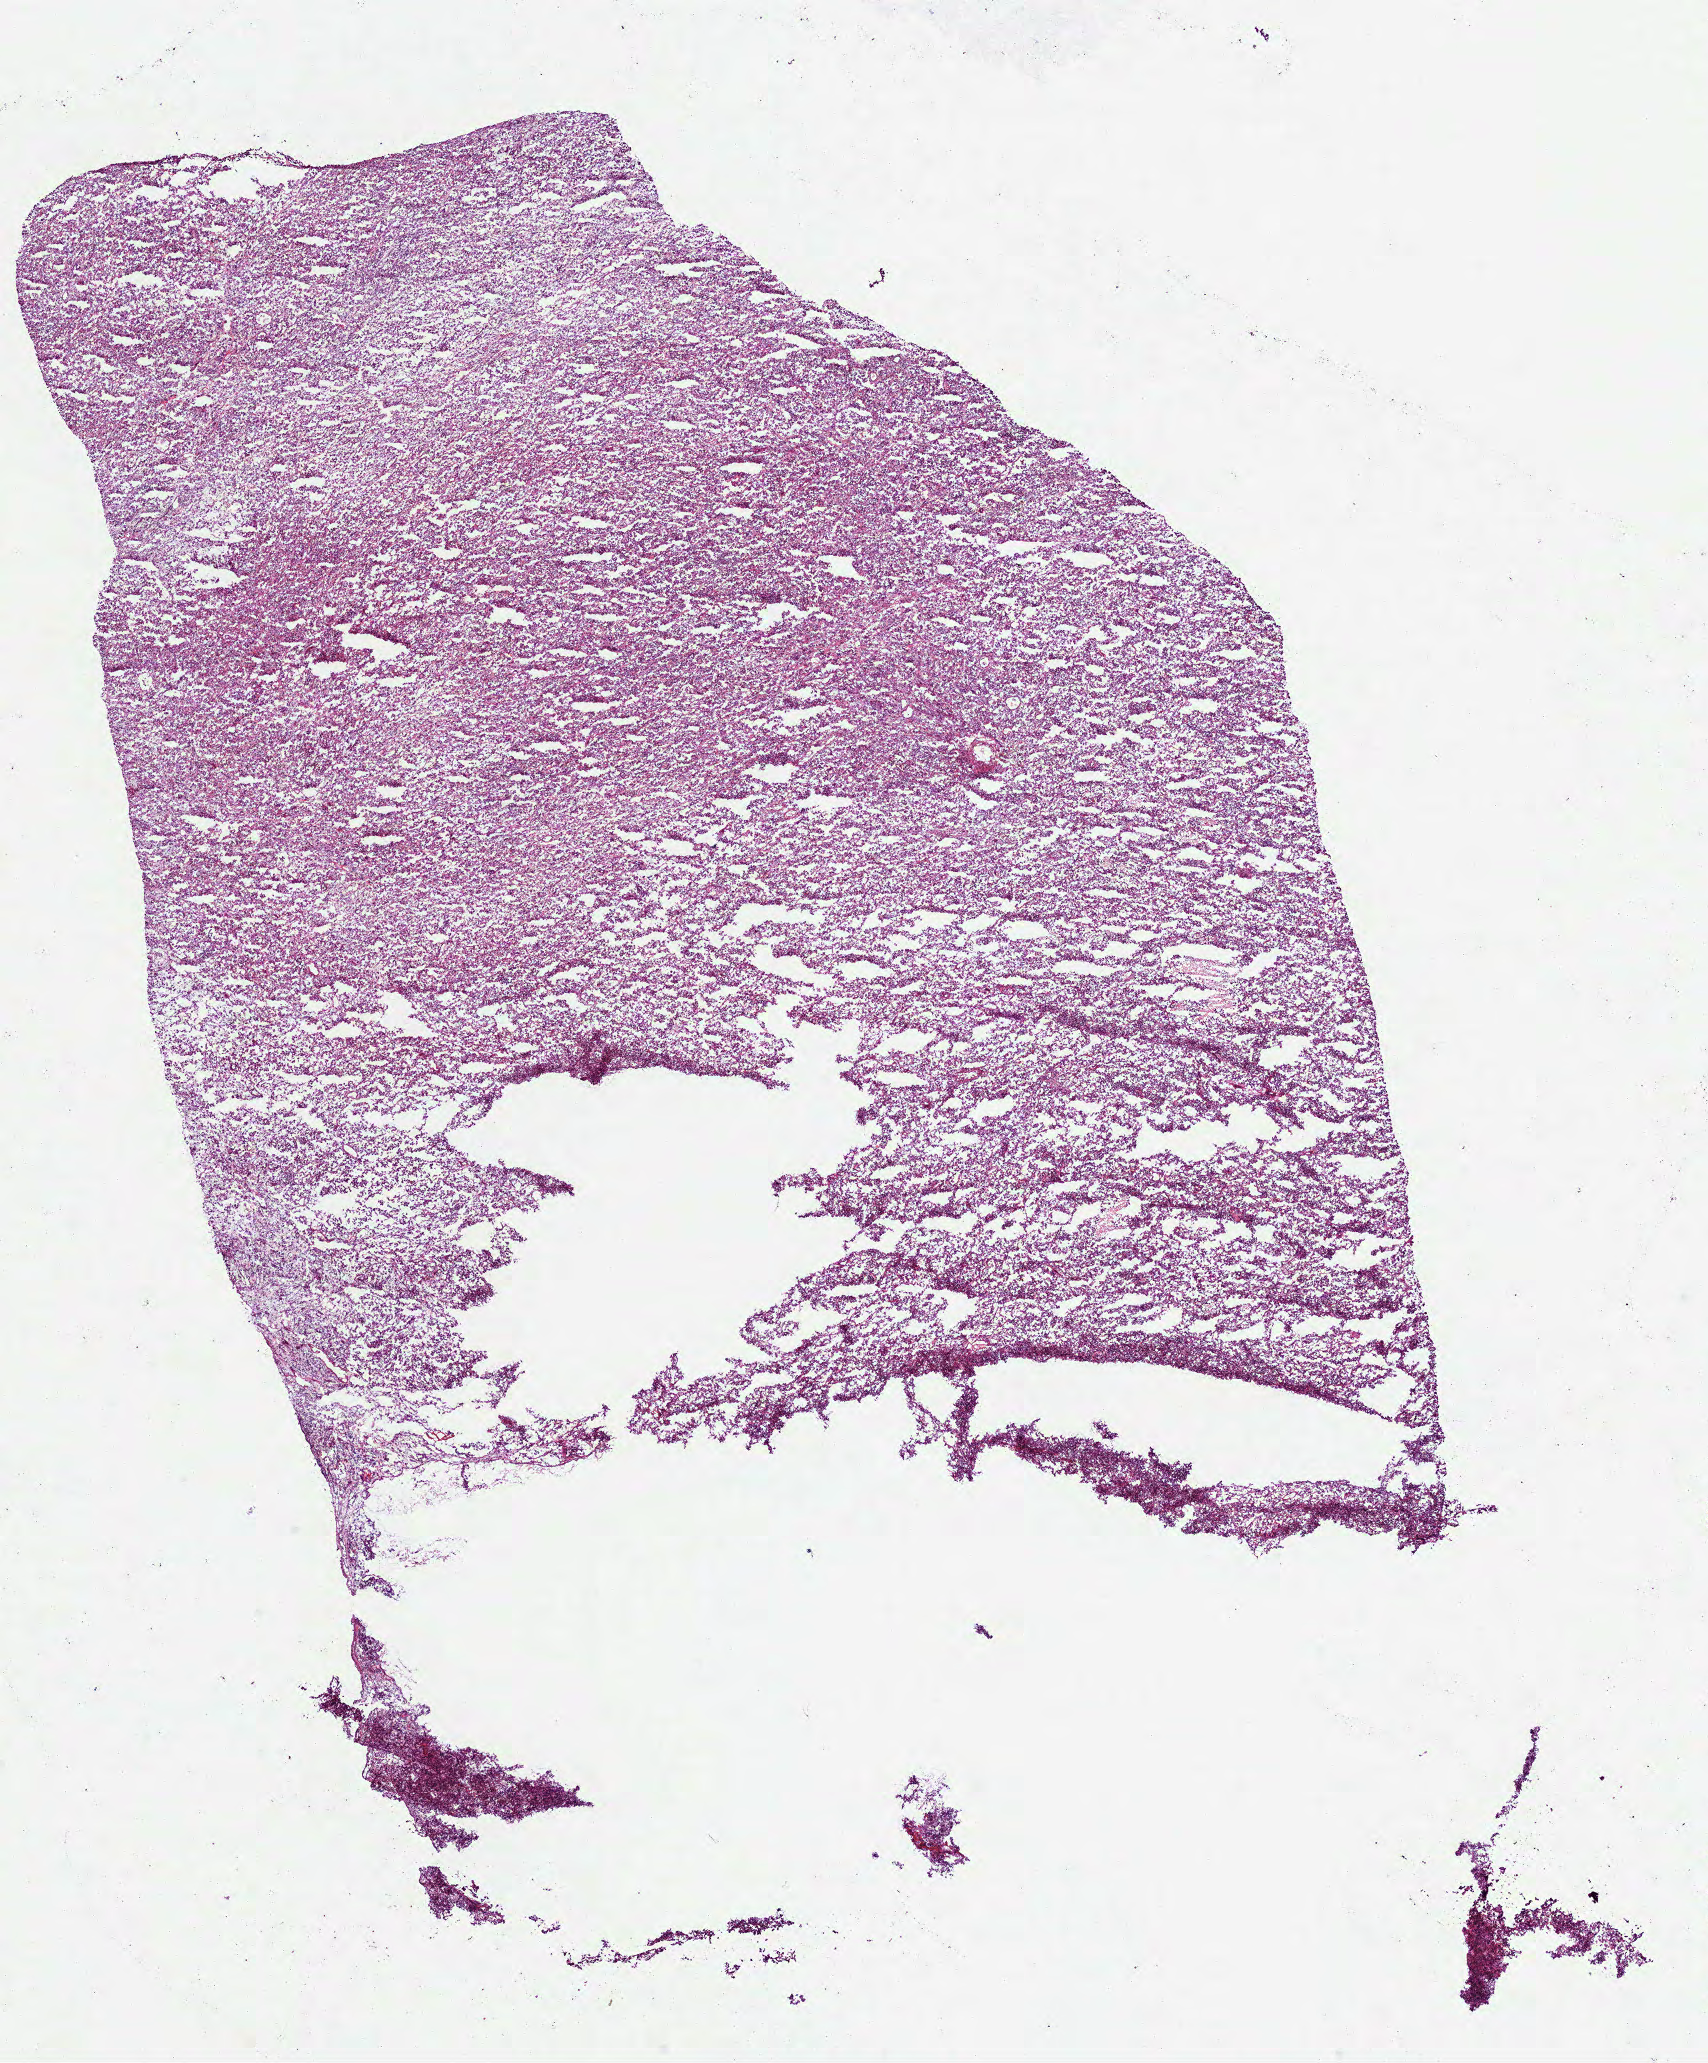
H&E-stained whole-slide image — a low-resolution overview of the entire scanned area, about 13.8 x 16.6 mm; frozen section; primary tumour sample from the kidney. Male, age 54 years at initial diagnosis.
Histologic diagnosis: Renal cell carcinoma, chromophobe type.